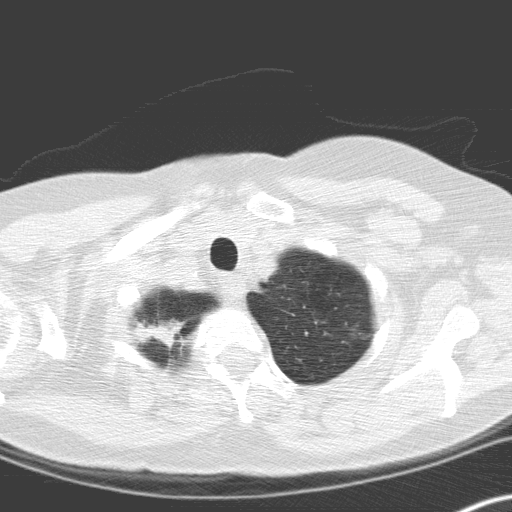
Low-dose screening chest CT, one axial slice; slice 145 of 166 in the series (ordered by position); lung window (W 1500 / L -600 HU); 3.2 mm slice thickness; 512 × 512 image matrix.
Annotated regions visible in this slice (expert manual segmentation):
- lesion 1 (tumor, upper lobe of right lung): bounding box <136,320,179,347> (left, top, right, bottom; pixels)